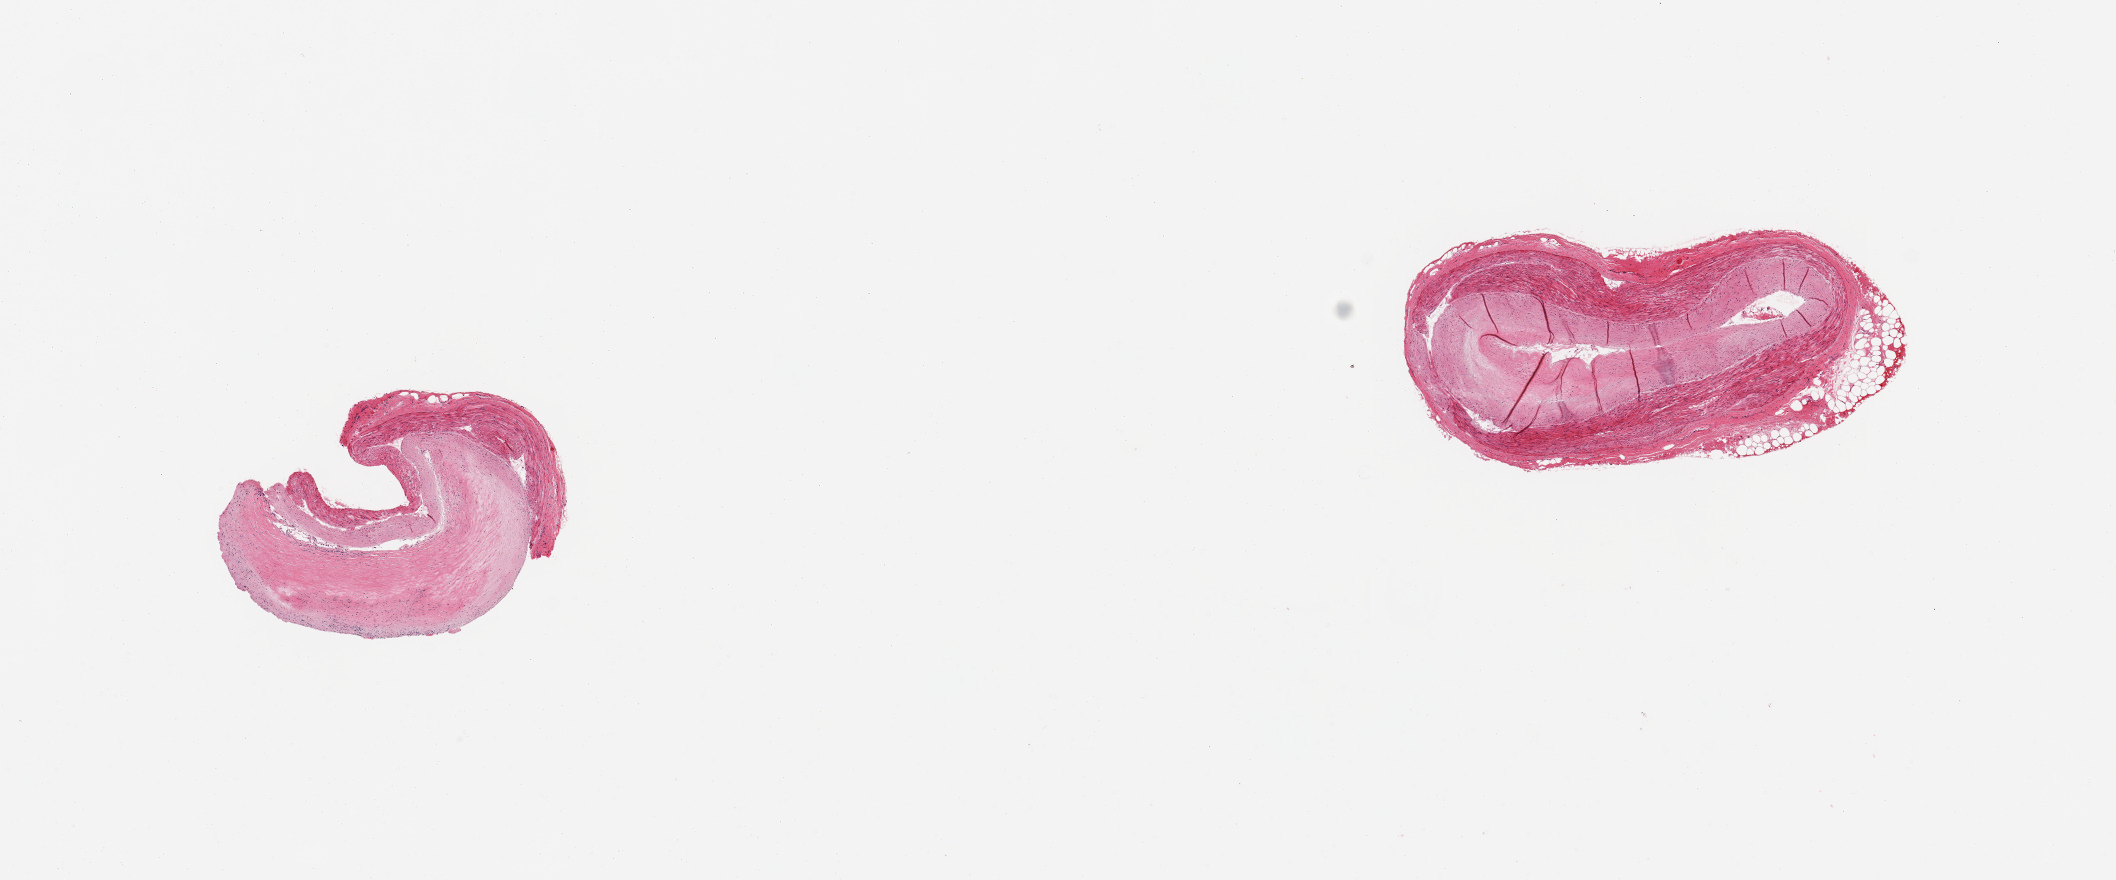
Whole-slide image, hematoxylin and eosin (H&E) stain, brightfield — a low-resolution overview of the entire scanned area, about 16.7 x 7.0 mm (from a 20x scan), PAXgene-fixed paraffin-embedded (PFPE) section, target tissue: coronary artery, tissue donor sample. Donor: male.
• reviewer comment on this tissue sample: 2 pieces; thick intimal plaques up to 1 mm thick; focus of adventitial fat (20%) on one